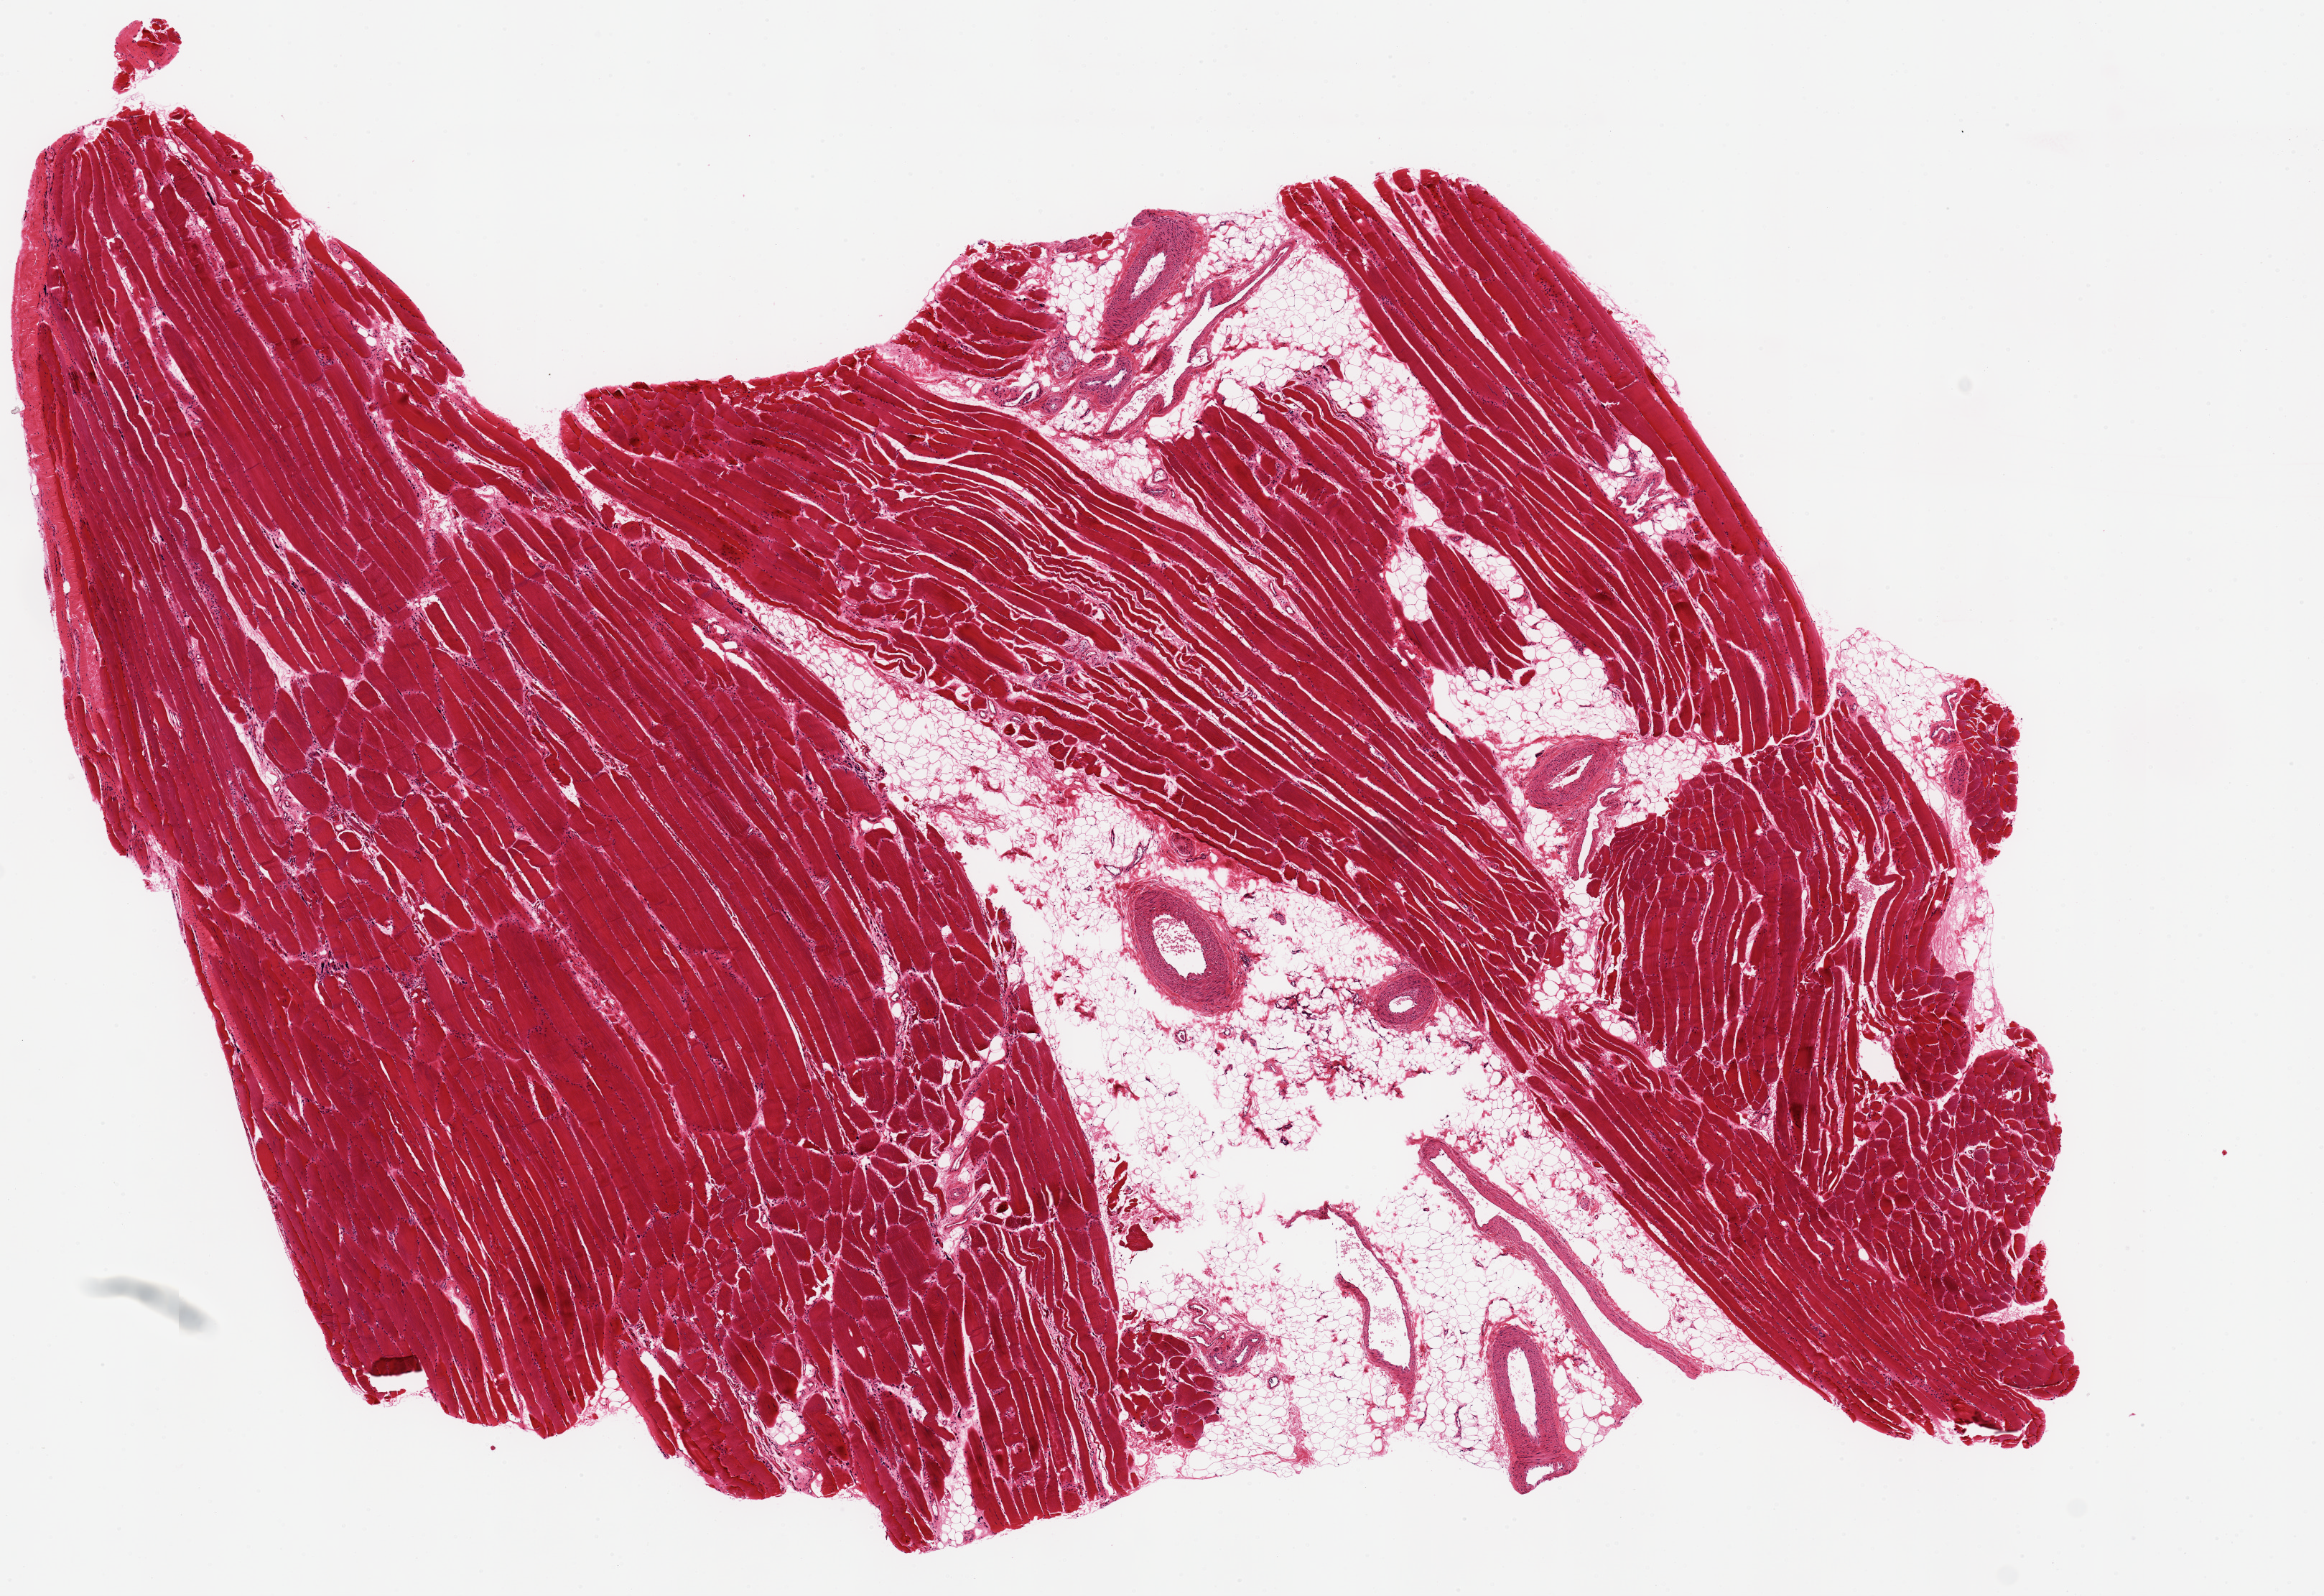
Hematoxylin and eosin (H&E) whole-slide image, whole scanned area (about 12.8 x 8.8 mm) shown as a low-resolution overview; PAXgene-fixed paraffin-embedded (PFPE) section; target tissue: skeletal muscle; donor tissue sample.
- review note (as recorded): ~25% adipose tissue centrally